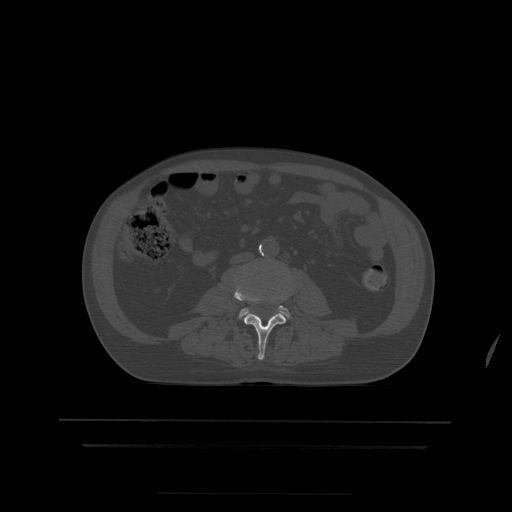
CT including the spine, one axial slice. Bone window (W 1800 / L 400 HU). 512 × 512 image matrix. Patient age 68 years. From the clinical record (not read from this slice): primary cancer: urothelial.
Annotated regions visible in this slice (semi-automatic segmentation, software-assisted and operator-edited):
- L3 vertebra: box from (x=234, y=285) to (x=286, y=360) px
- L4 vertebra: (x=240, y=298)–(x=290, y=317)